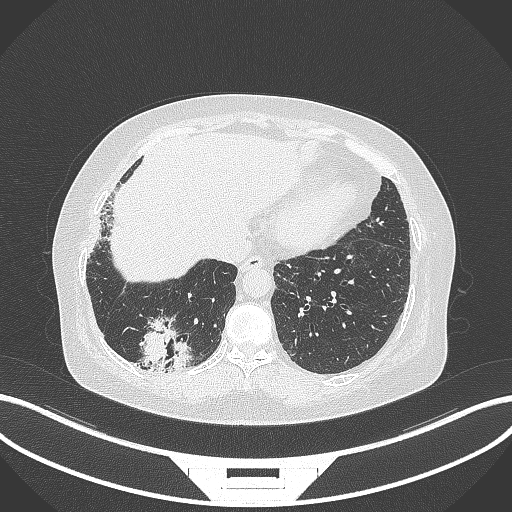
Chest CT, one axial slice; position 43 of 296 along the scan axis; reconstruction kernel B70f; 120 kVp; lung window (W 1500 / L -600 HU); 1 mm slice thickness; 512 × 512 image matrix. Female patient, age 65 years. From the clinical record (not read from this slice): clinical TNM (as recorded): T2b N1 M0; histopathological grade: G1.
Structures marked on this image (rectangle marked by the reading radiologist):
- lung tumour (recorded histology: adenocarcinoma): bounding box [x1, y1, x2, y2] px = [133, 313, 196, 371]